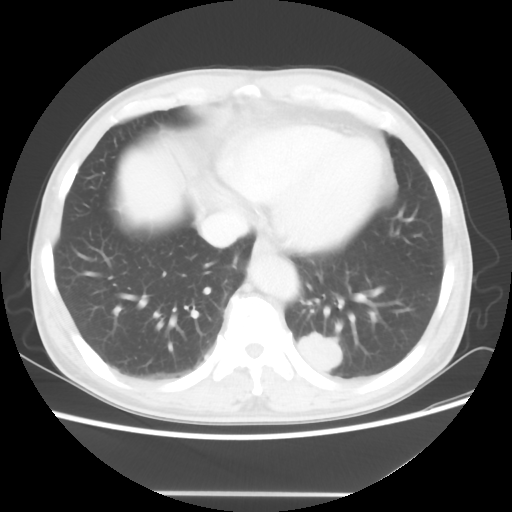
Chest CT, one axial slice. Slice 16 of 60 in the series (ordered by position). Reconstruction kernel STANDARD. Lung window (W 1500 / L -600 HU). 5 mm slice thickness. 512 × 512 image matrix, field of view 360 × 360 mm. Patient: male, 55 years. Case-level facts recorded for this patient, not image findings: clinical TNM (as recorded): T1c N3 M0.
Structures marked on this image (rectangle marked by the reading radiologist):
- lung tumour (recorded histology: small cell carcinoma): box from (x=292, y=330) to (x=345, y=375) px